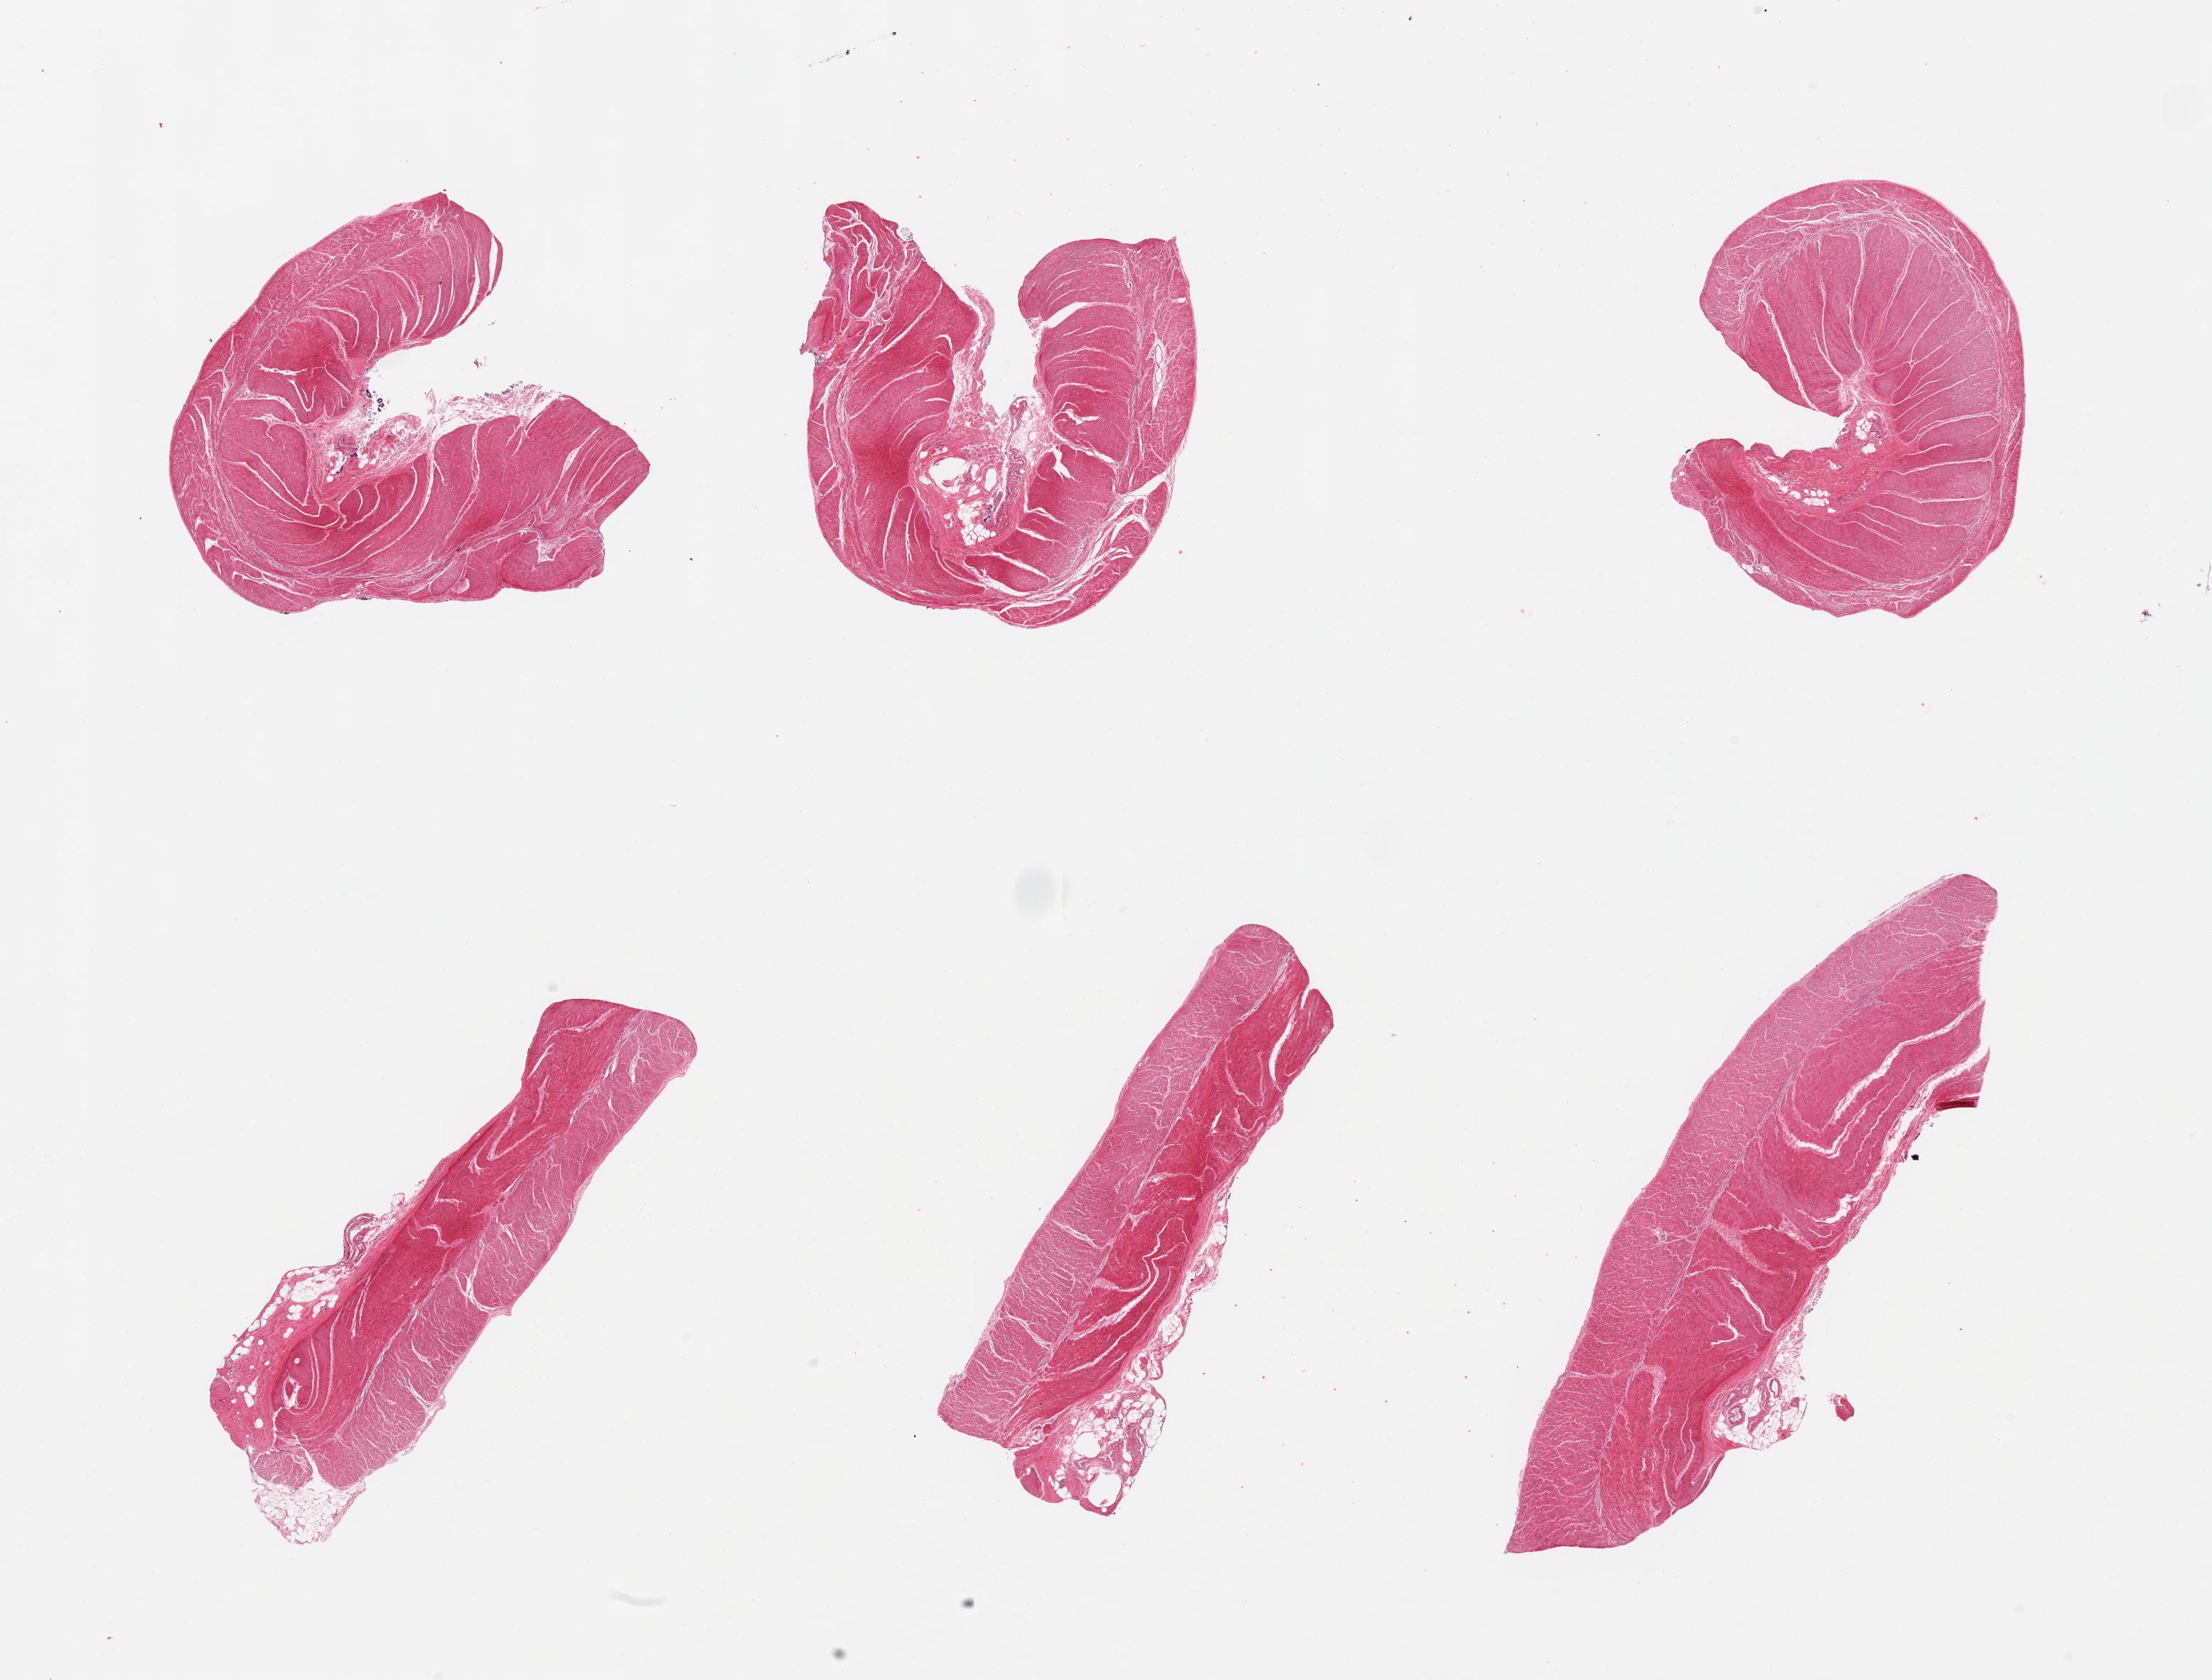
Digitized H&E-stained section — low-resolution overview of the scanned area, about 24.6 x 18.7 mm (slide scanned at 20x), PAXgene-fixed paraffin-embedded (PFPE) section, target tissue: sigmoid colon, tissue donor sample. Female donor.
Reviewer comment on this tissue sample: 6 pieces; target muscularis.